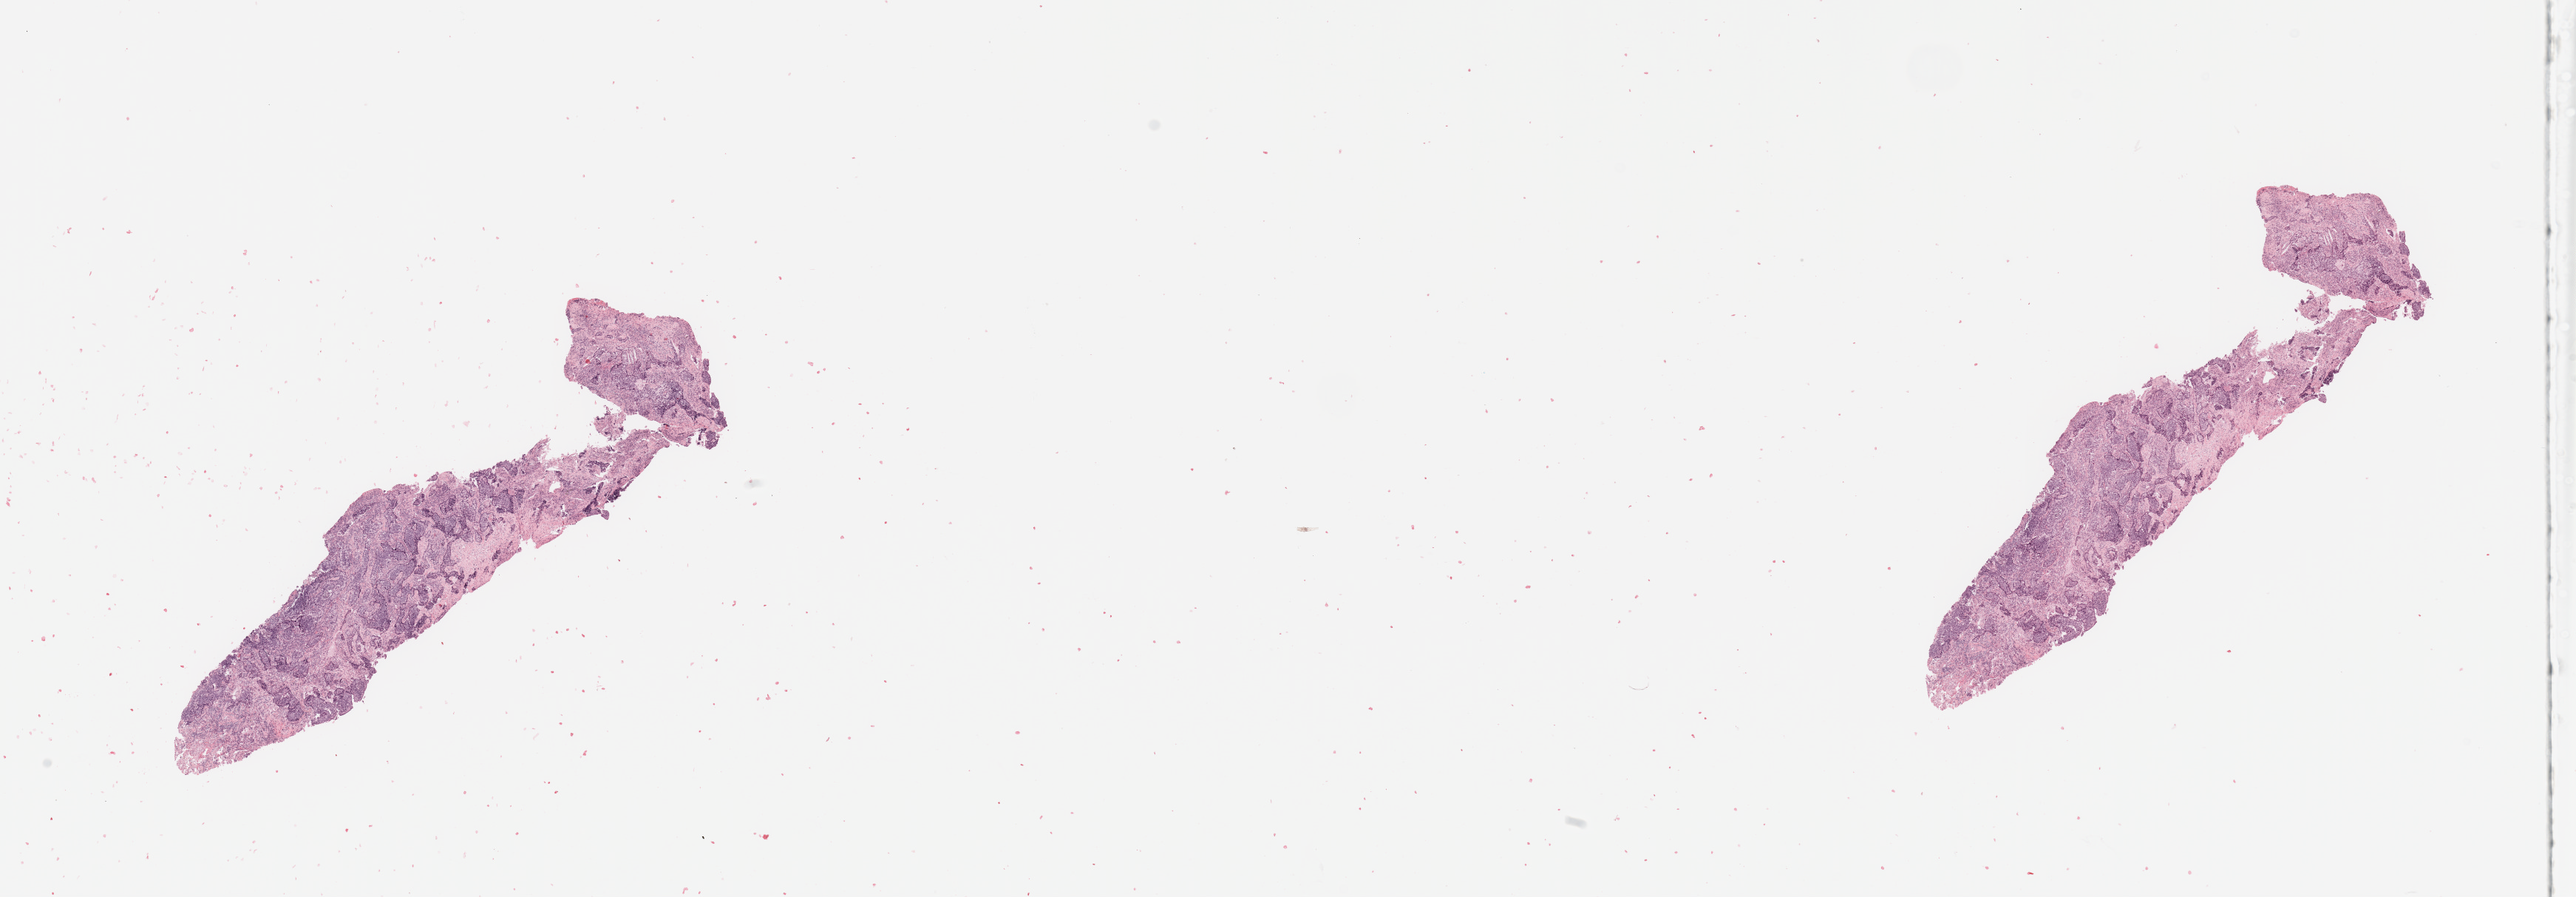
Digitized H&E tissue section (whole slide), low-resolution overview of the scanned area, about 27.6 x 9.6 mm; tumour tissue sample, sampled site: lung. 71-year-old male patient. Histologic grade: G2 (moderately differentiated). Pathologist review of this section (percent, as recorded): tumour nuclei 75%, necrosis 5%.
* AJCC pathologic stage: IA
* primary tumour site (as recorded): left upper lobe
* histologic diagnosis: Adenocarcinoma, NOS